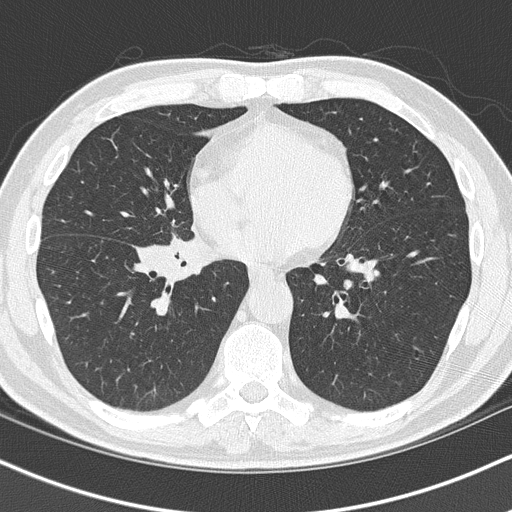
Chest CT (low-dose screening protocol), one axial image, baseline screening round, lung window (W 1500 / L -600 HU), 2 mm slice thickness, 120 kVp, slice 54 of 151 in the series. Male participant, aged 55 years at enrolment. Current smoker at enrolment.
Lesion marked by an expert reader, box from (x=133, y=226) to (x=239, y=306) px. Reader record for this screening exam (exam-level; its link to the box is not recorded): non-calcified nodule or mass ≥4 mm, right lower lobe, 6 × 5 mm, spiculated (stellate) margins, soft tissue attenuation. Official screen result: positive, change unspecified: nodule(s) >= 4 mm or enlarging nodule(s), mass(es), or other non-specific abnormalities suspicious for lung cancer.